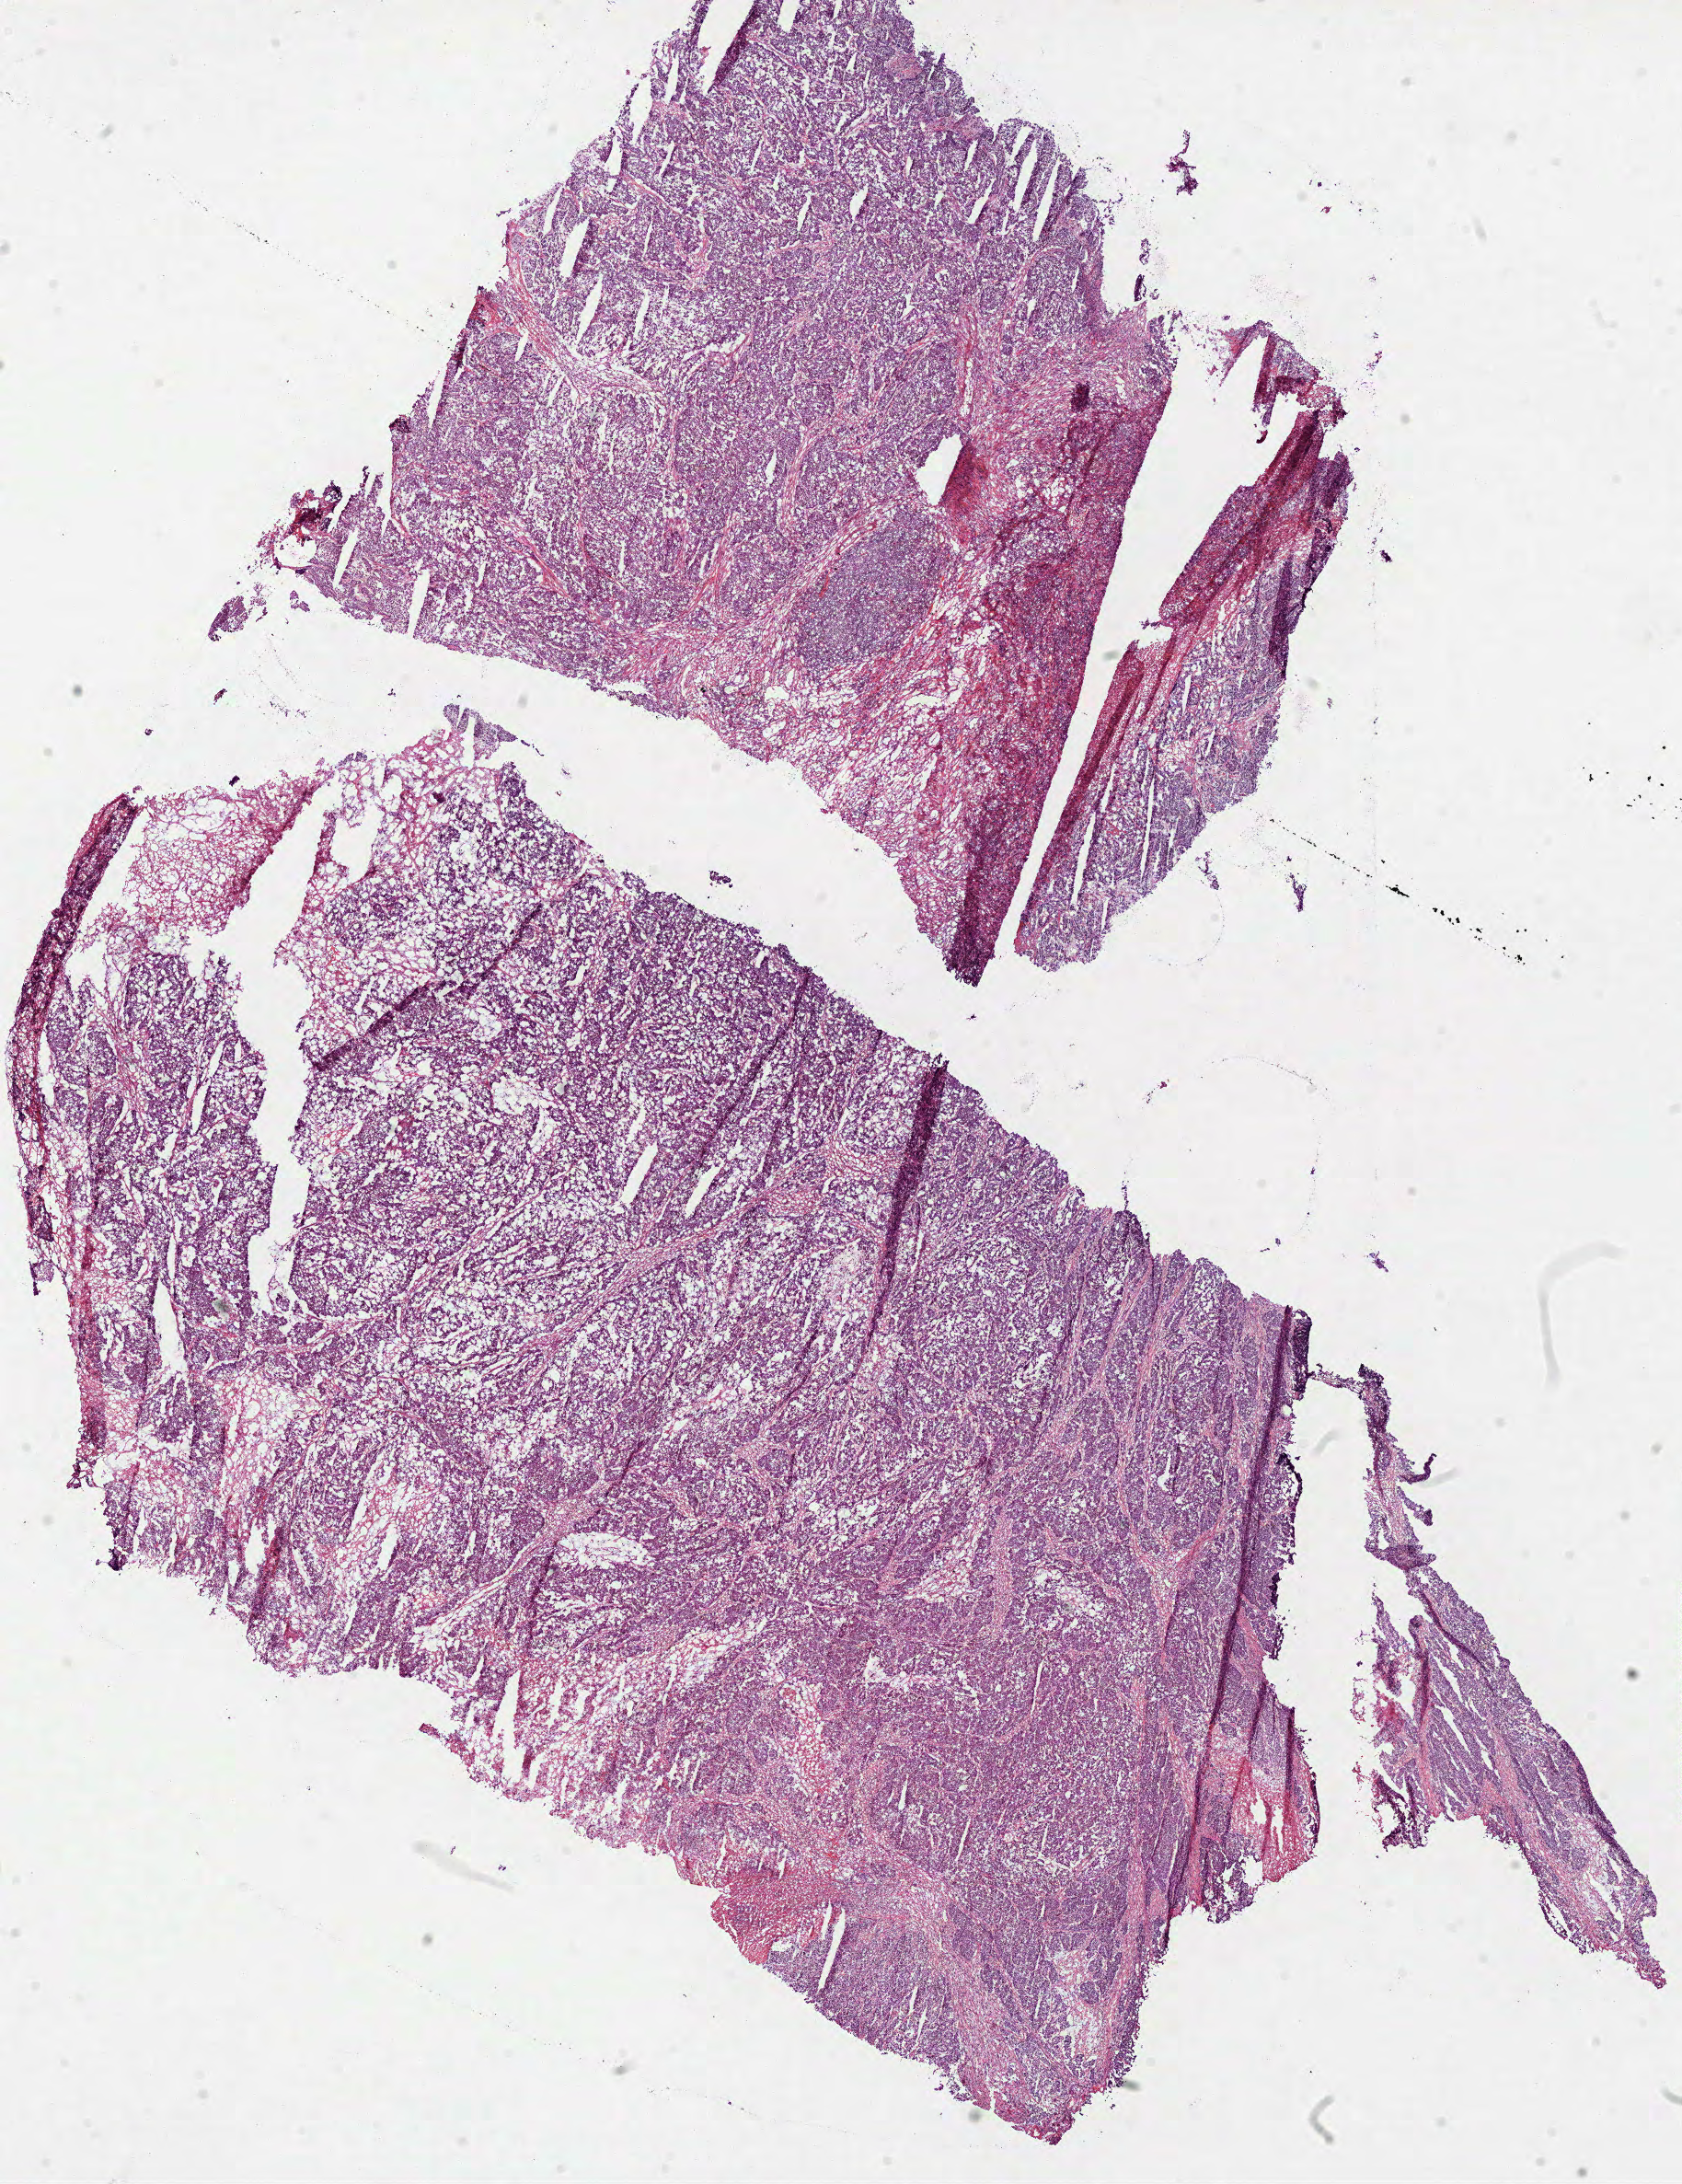
Whole-slide histology image, Hematoxylin and eosin (H&E) stained — low-resolution overview of the scanned area, about 14.7 x 19.1 mm (from a 40x scan); frozen section from the top of the tissue portion; sample: primary tumour, colon. Patient: female, age at initial diagnosis 77 years.
Diagnosis: Adenocarcinoma, NOS.